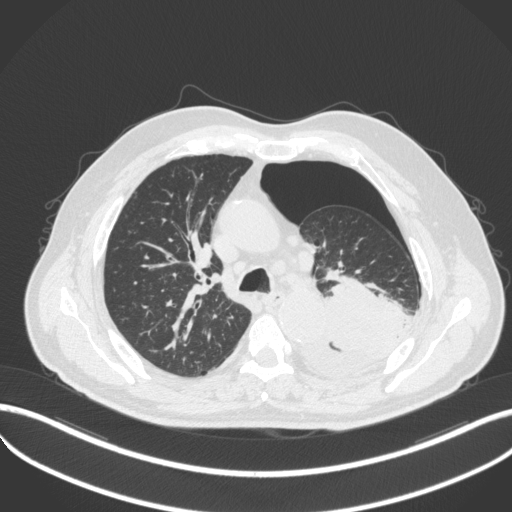
Chest CT, one axial slice. Position 349 of 466 along the scan axis. Lung window (W 1500 / L -600 HU). 1 mm slice thickness. 512 × 512 image matrix, field of view 400 × 400 mm. Male patient, age 76 years. From the clinical record (not read from this slice): clinical TNM (as recorded): T3 N0 M1b.
Outlined on this slice (rectangle marked by the reading radiologist):
- lung tumour (recorded histology: adenocarcinoma): bounding box [x1, y1, x2, y2] px = [294, 282, 409, 378]